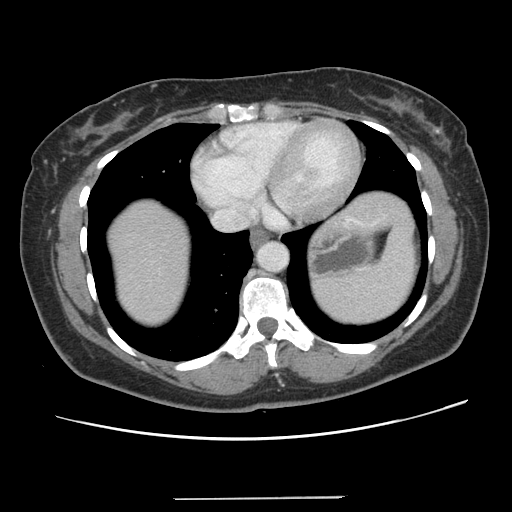
Contrast-enhanced abdominal CT, one axial slice. Position 123 of 141 along the scan axis. 120 kVp. Intravenous contrast given. Soft-tissue window (W 400 / L 40 HU). 512 × 512 image matrix. Female patient, age 53 years. From the clinical record (not read from this slice): diagnosis: colorectal cancer liver metastases, imaged before liver resection; multiple liver metastases: no; largest metastasis: 14.5 cm; disease in both lobes: yes.
Annotated regions visible in this slice (expert manual segmentation):
- liver: box from (x=105, y=191) to (x=407, y=327) px
- planned liver remnant (the part of the liver to remain after resection): (x=106, y=215)–(x=190, y=327)